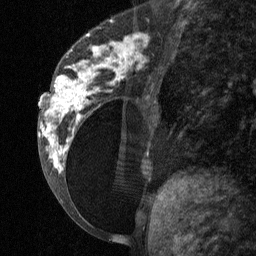
Breast MRI (dynamic contrast-enhanced), one sagittal slice. Slice 27 of 64 in the series (ordered by position). Dynamic contrast-enhanced study with each time point stored as its own series, time point 2 of 3 at this slice position (early post-contrast, ordered by acquisition time). 1.5 T. TE 4.8 ms, TR 27 ms. 2 mm slice thickness. 256 × 256 image matrix, field of view 180 × 180 mm. Female patient, age 34 years. Case-level facts recorded for this patient, not image findings: setting: breast cancer imaged before/during neoadjuvant chemotherapy; receptor status: HR-positive, HER2-negative.
Structures marked on this image (semi-automatic segmentation, software-assisted and operator-edited):
- analysis volume of interest (the breast-tissue region the enhancement analysis was run in; not a lesion): box from (x=41, y=23) to (x=157, y=197) px
- tumour enhancement mask (voxels above the 90 % enhancement threshold inside the analysis volume of interest): (x=41, y=34)–(x=144, y=171)